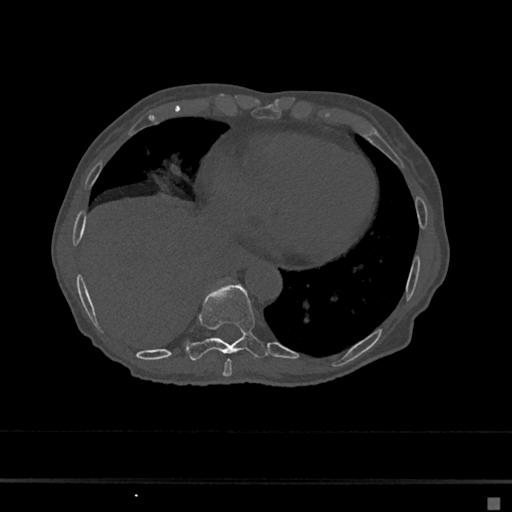
CT including the spine, one axial slice. Slice 275 of 797 in the series (ordered by position). Reconstruction kernel Br40s/3. 120 kVp. Bone window (W 1800 / L 400 HU). 512 × 512 image matrix. Patient: female, 68 years. From the clinical record (not read from this slice): primary cancer: renal.
Structures marked on this image (semi-automatically segmented with operator editing):
- T8 vertebra: bounding box (x1, y1, x2, y2) in pixels: (223, 359, 232, 377)
- T9 vertebra: (186, 283, 269, 361)